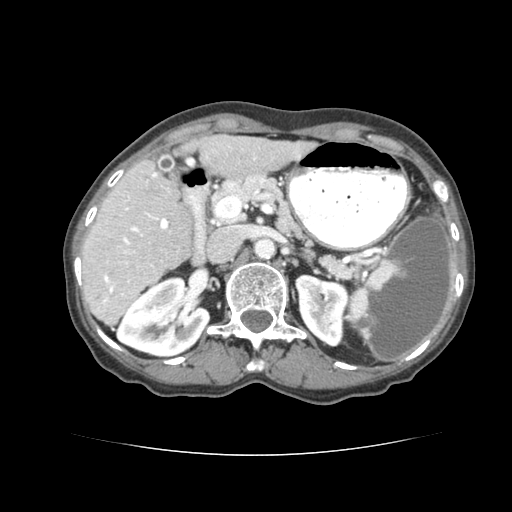
Contrast-enhanced abdominal CT (liver protocol), one axial slice. Position 38 of 77 along the scan axis. 120 kVp. Soft-tissue window (W 400 / L 40 HU). 512 × 512 image matrix, field of view 340 × 340 mm. From the clinical record (not read from this slice): diagnosis: hepatocellular carcinoma (patient treated with transarterial chemoembolisation; whether this scan precedes or follows treatment is not stated here); TNM stage (as recorded): Stage-I; Child-Pugh class: A; tumour nodularity: uninodular.
Annotated regions visible in this slice (semi-automatic segmentation, software-assisted and operator-edited):
- liver parenchyma outside the tumour (the mass and vessels are separate outlines, so this box may not span the whole liver): box from (x=80, y=138) to (x=314, y=322) px
- liver vessels: (x=99, y=157)–(x=273, y=303)